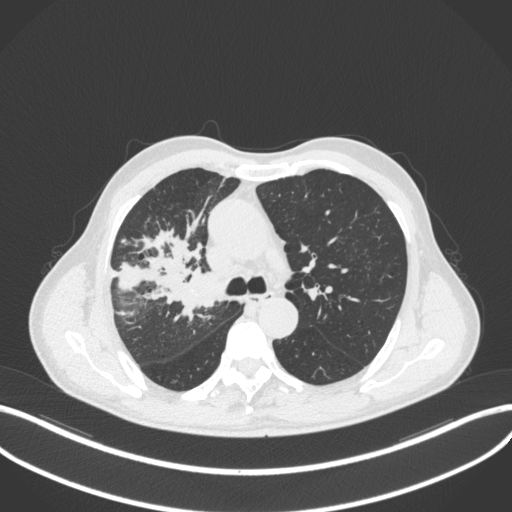
Chest CT, one axial slice. Slice 325 of 490 in the series (ordered by position). Reconstruction kernel B31f. 120 kVp. Lung window (W 1500 / L -600 HU). 1 mm slice thickness. 512 × 512 image matrix, field of view 400 × 400 mm. Patient: male, 69 years. From the clinical record (not read from this slice): clinical TNM (as recorded): T2a N0 M0.
Outlined on this slice (bounding box drawn by a radiologist):
- lung tumour (recorded histology: adenocarcinoma): bounding box [x1, y1, x2, y2] px = [173, 271, 220, 314]